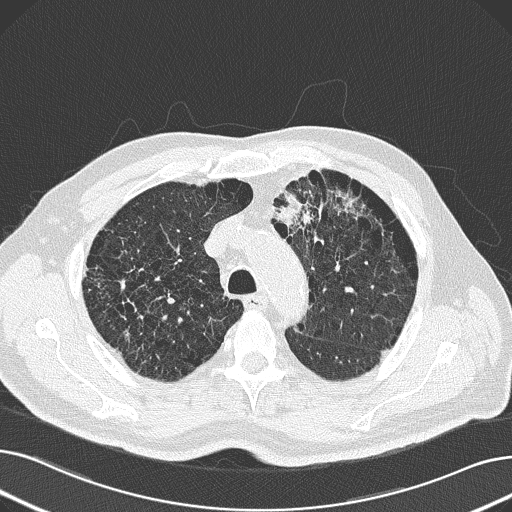
Axial slice from a low-dose chest CT screening exam. Baseline annual screen. Lung window (W 1500 / L -600 HU). Lung (sharp) reconstruction kernel (B50f). Slice 50 of 165 in the series. 512 × 512 image matrix. Male, age 69 years at enrolment. Former smoker at enrolment.
- Lesion marked by an expert reader, bounding box <223,151,378,256> (left, top, right, bottom; pixels).
- The exam's reader record, not a measurement of the box and not confirmed to be the same lesion: non-calcified nodule or mass ≥4 mm, left upper lobe, 6 × 10 mm, spiculated (stellate) margins, soft tissue attenuation.
- Lung cancer was diagnosed 20 days after this screen: non-small cell carcinoma, left upper lobe, poorly differentiated (G3), stage IB (AJCC 6th edition), 100 mm at pathology.